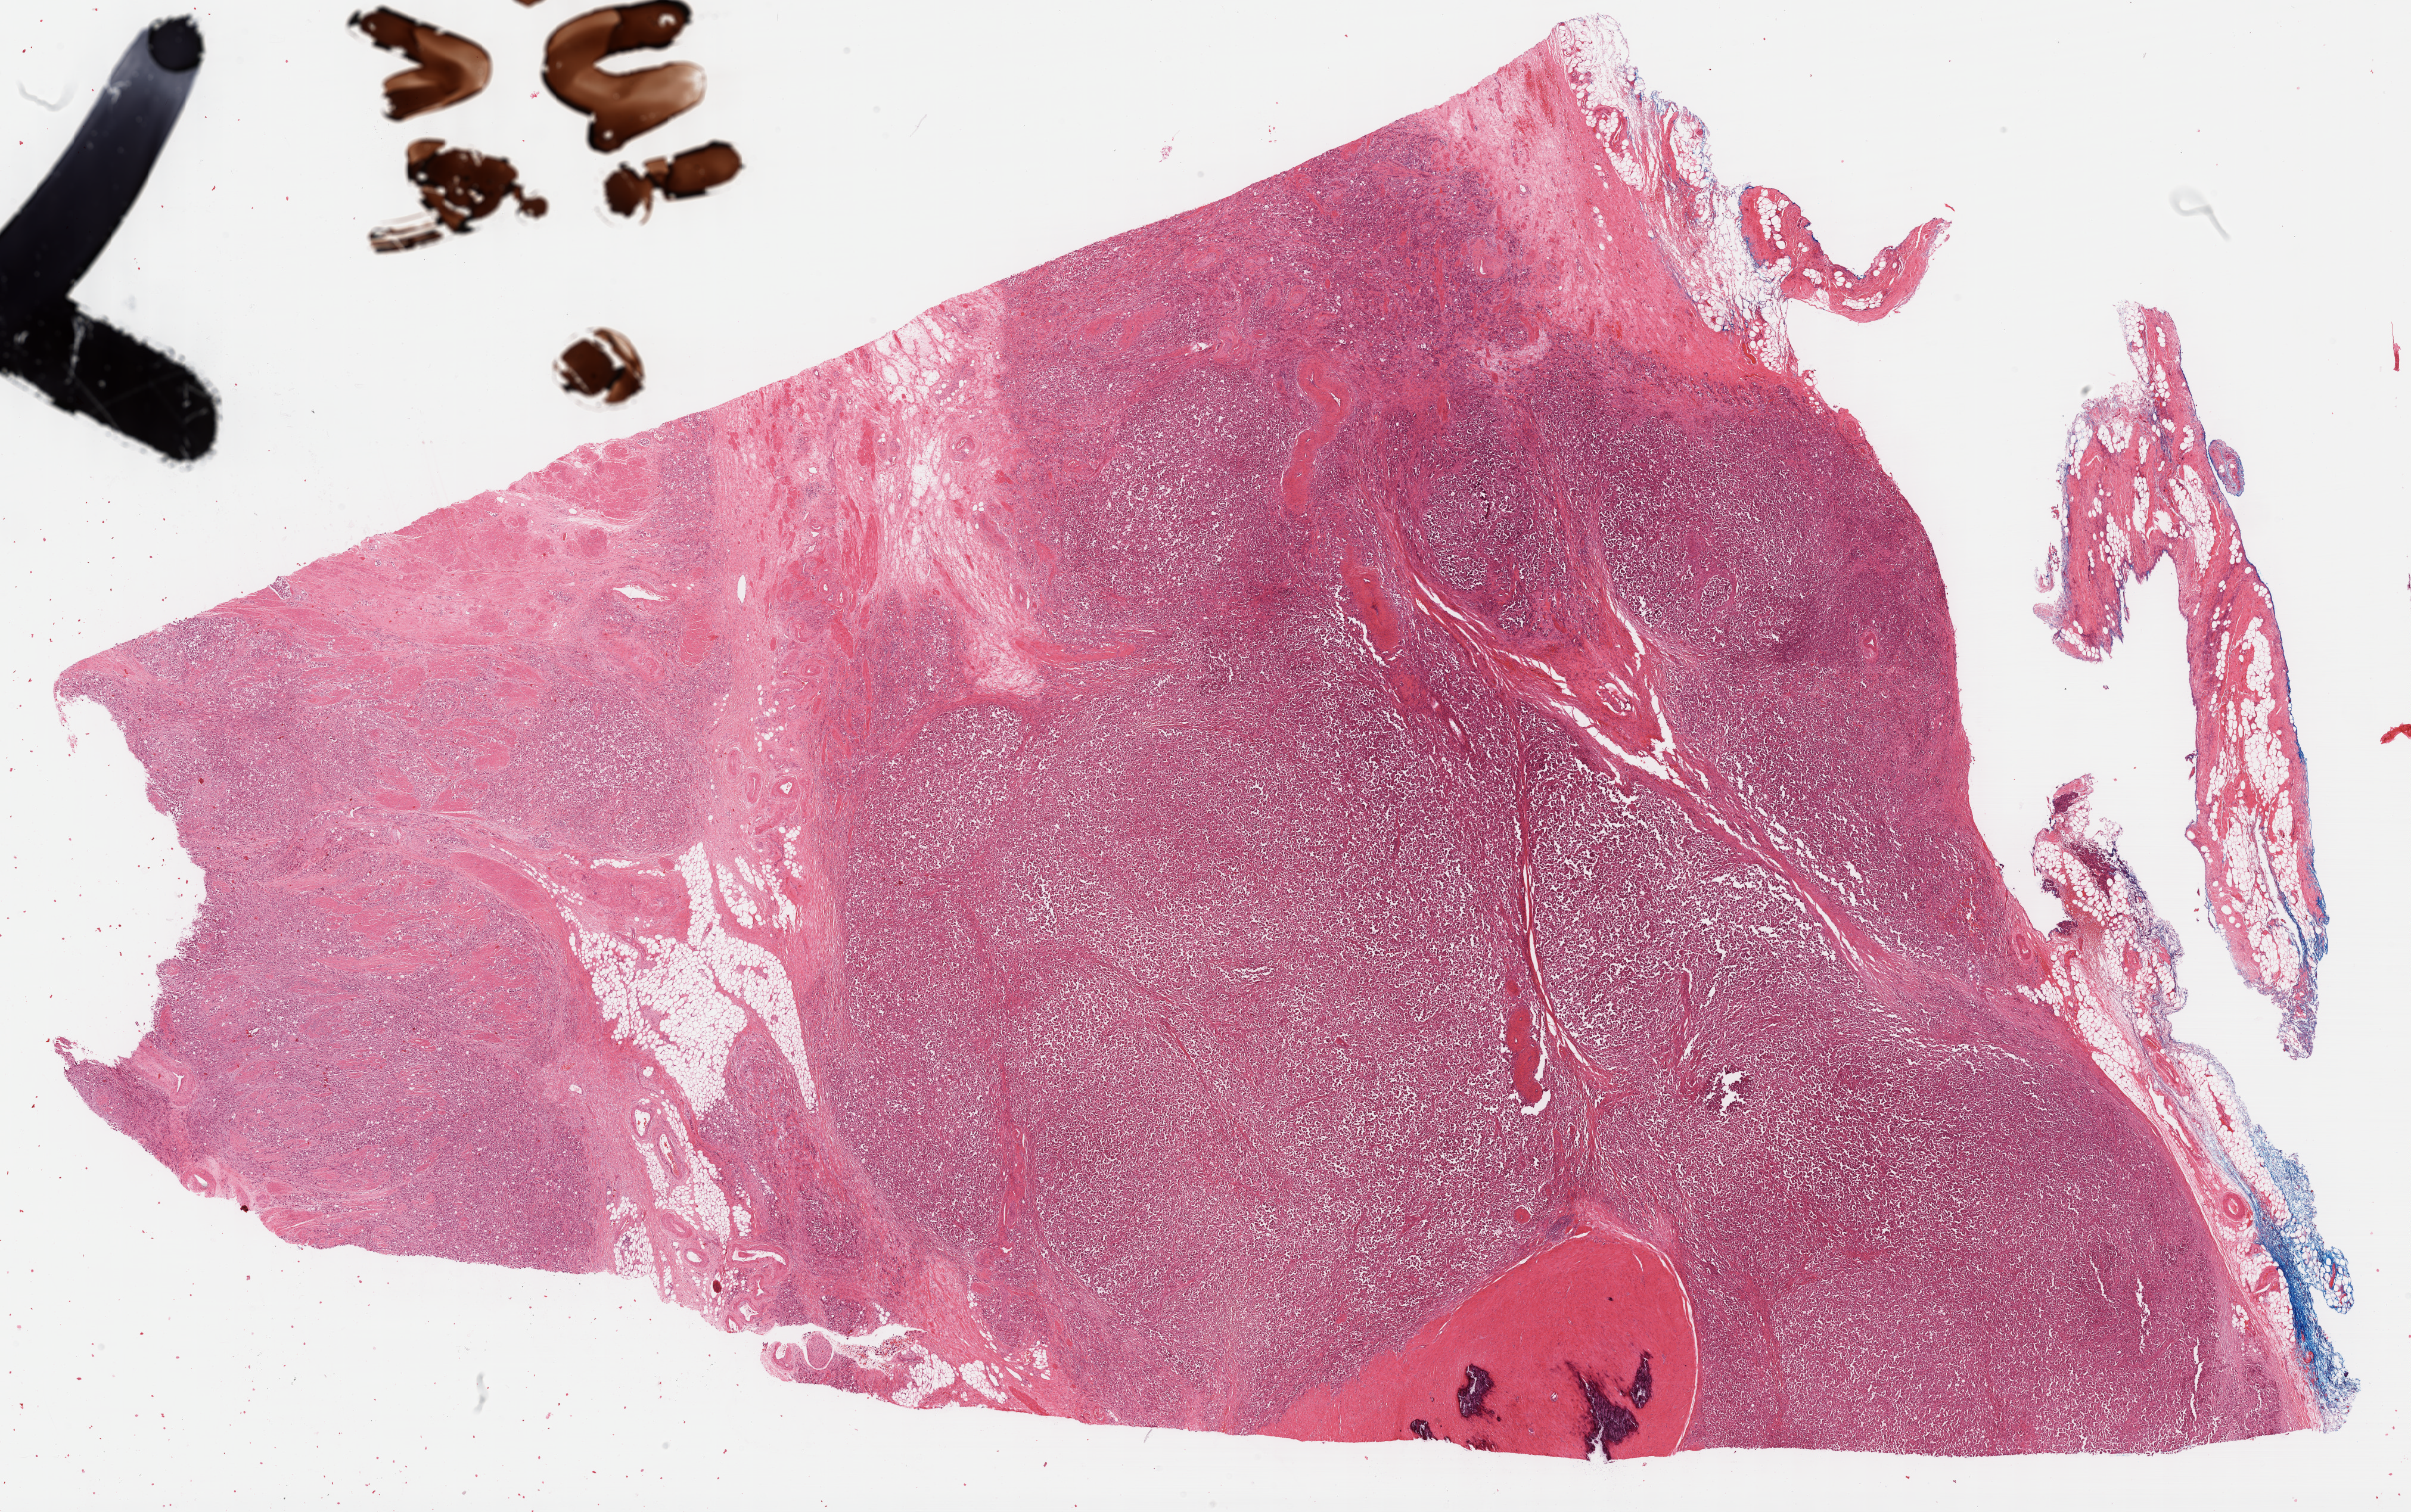
H&E-stained whole-slide image, a low-resolution overview of the entire scanned area, about 32.7 x 20.5 mm. Formalin-fixed paraffin-embedded (FFPE) diagnostic section. Primary tumour sample from the bladder. Male patient; age at initial diagnosis 70 years. Histologic grade: high grade.
* TNM: T3a NX MX
* diagnosis: Transitional cell carcinoma (posterior wall of bladder)
* AJCC pathologic stage: III (6th edition)